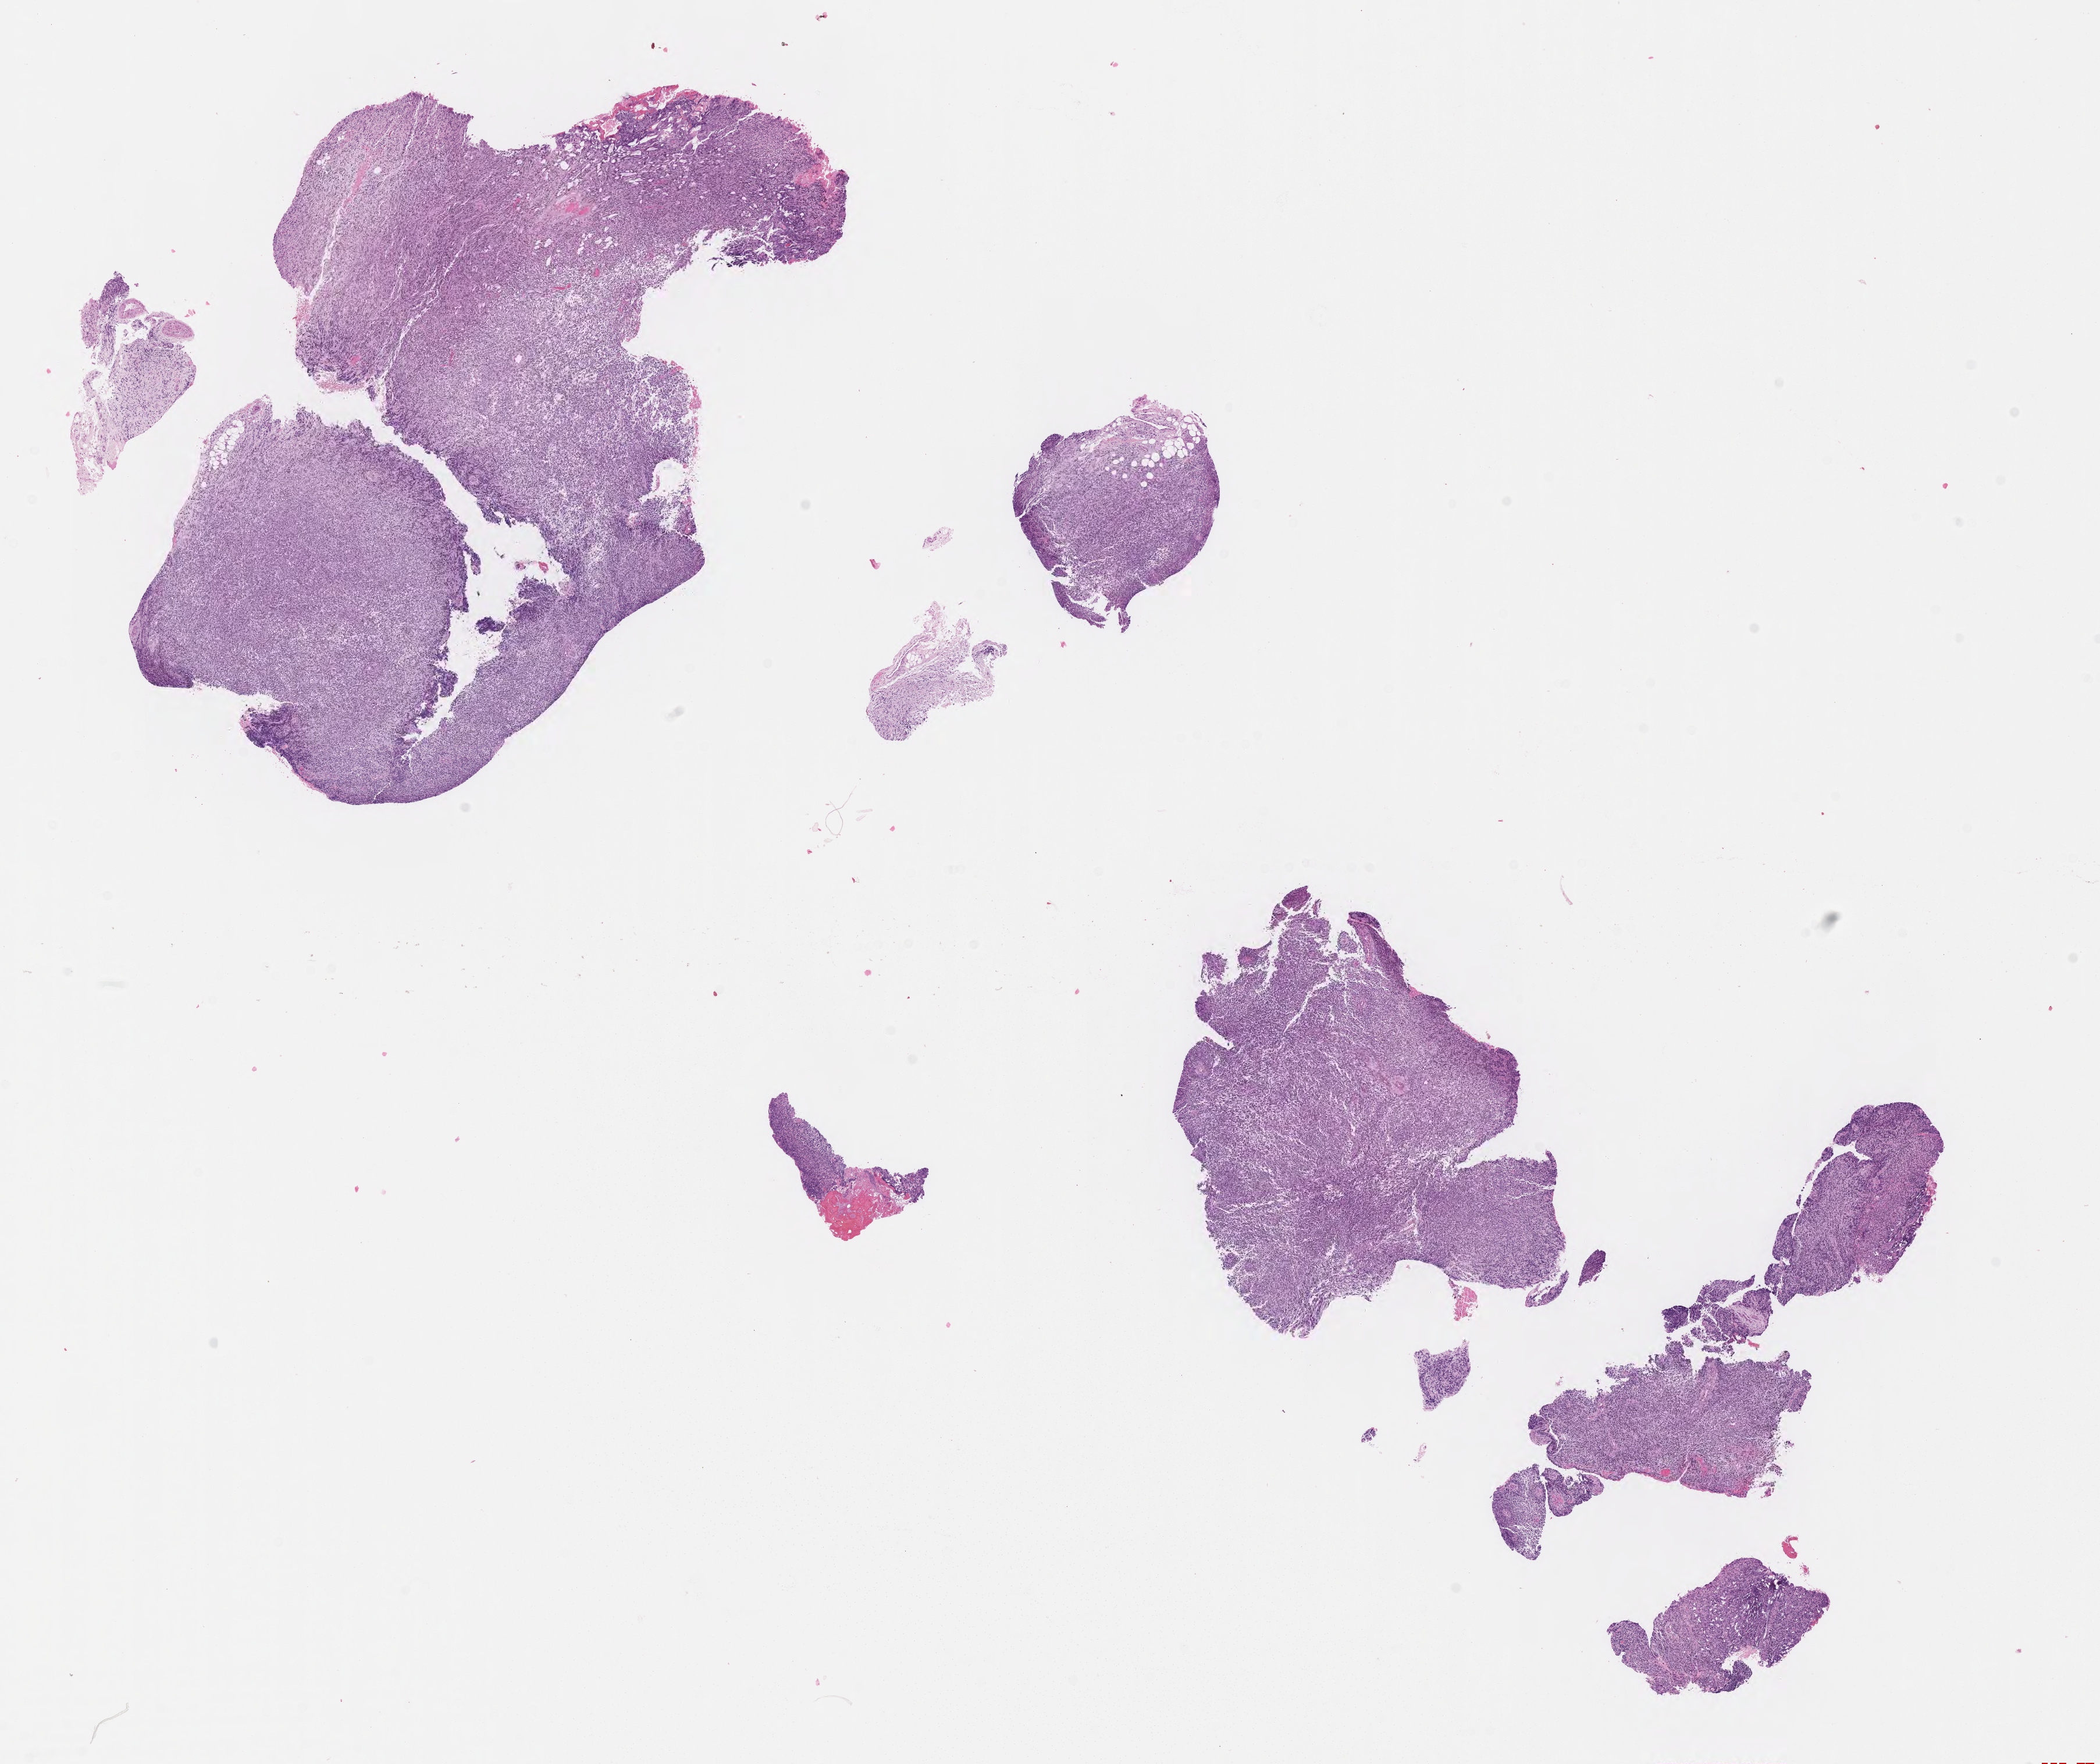
Whole-slide image, H&E stain of tumor tissue, a low-resolution overview of the entire scanned area, about 14.6 x 12.3 mm, formalin-fixed paraffin-embedded section, site: orbit, right. Female patient, age at diagnosis 6.3 years.
Diagnosis: rhabdomyosarcoma; histological classification: spindle cell rhabdomyosarcoma.